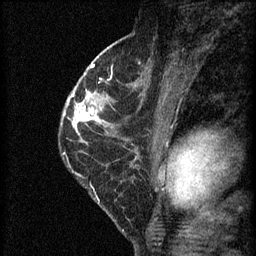
Breast MRI (dynamic contrast-enhanced), one sagittal slice; position 36 of 60 along the scan axis; 3 images stored at this slice position (order not interpretable as contrast timing); 1.5 T; TE 4.2 ms, TR 8.2 ms; 2 mm slice thickness; 256 × 256 image matrix. Female patient, age 45 years.
Outlined on this slice (semi-automatically segmented with operator editing):
- analysis volume of interest (the breast-tissue region the enhancement analysis was run in; not a lesion): box from (x=62, y=98) to (x=104, y=139) px
- tumour enhancement mask (voxels above the 70 % enhancement threshold inside the analysis volume of interest): (x=76, y=102)–(x=99, y=129)